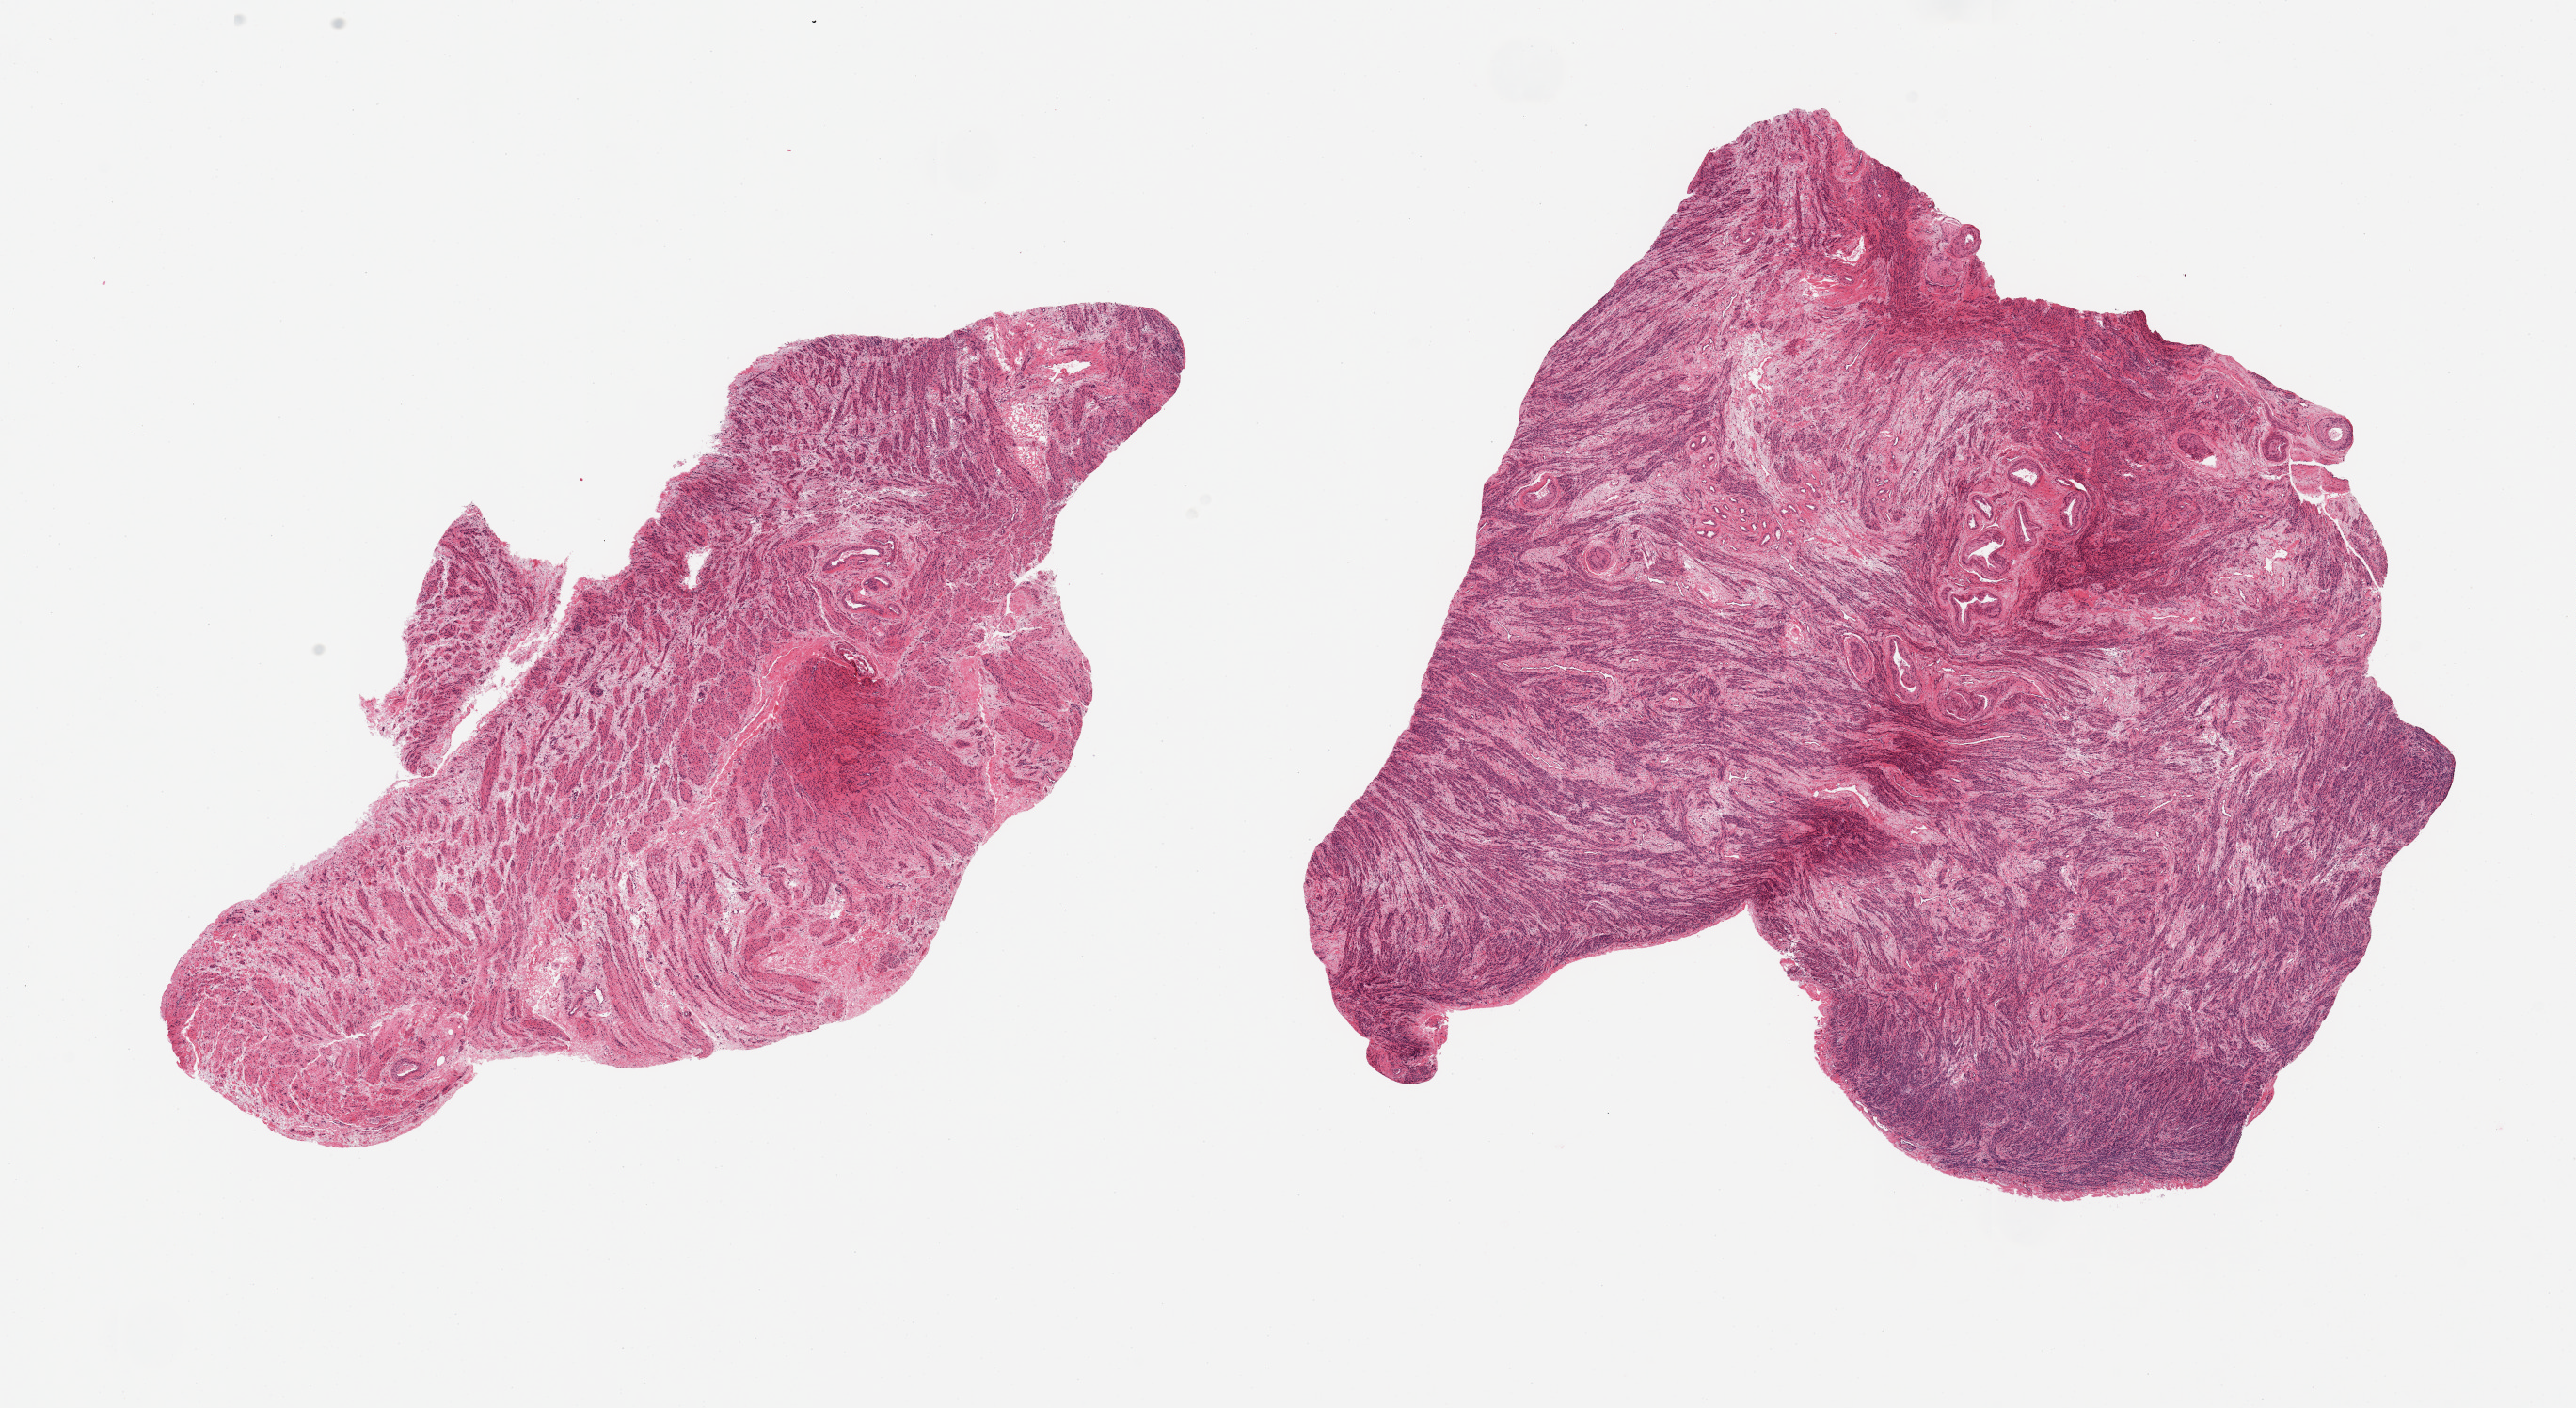
H&E whole-slide image — a low-resolution overview of the entire scanned area, about 21.7 x 11.8 mm; PAXgene-fixed paraffin-embedded (PFPE) section; target tissue: uterus; donor tissue sample. Donor sex: female.
Pathologist's review note for this sample: 2 pieces; all myometrium, no endometrium in this cut.